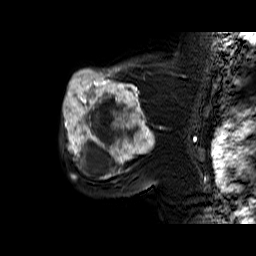
Breast MRI (dynamic contrast-enhanced), one sagittal slice. Position 44 of 60 along the scan axis. Dynamic contrast-enhanced series, time point 2 of 6 at this slice position (early post-contrast). 1.5 T. TE 6.4 ms, TR 32.9 ms. 4 mm slice thickness. 256 × 256 image matrix, field of view 200 × 200 mm. Female patient. From the clinical record (not read from this slice): setting: breast cancer imaged before/during neoadjuvant chemotherapy; receptor status: triple-negative.
Structures marked on this image (semi-automatically segmented with operator editing):
- analysis volume of interest (the breast-tissue region the enhancement analysis was run in; not a lesion): box from (x=61, y=65) to (x=159, y=174) px
- tumour enhancement mask (voxels above the 100 % enhancement threshold inside the analysis volume of interest): (x=63, y=65)–(x=155, y=174)